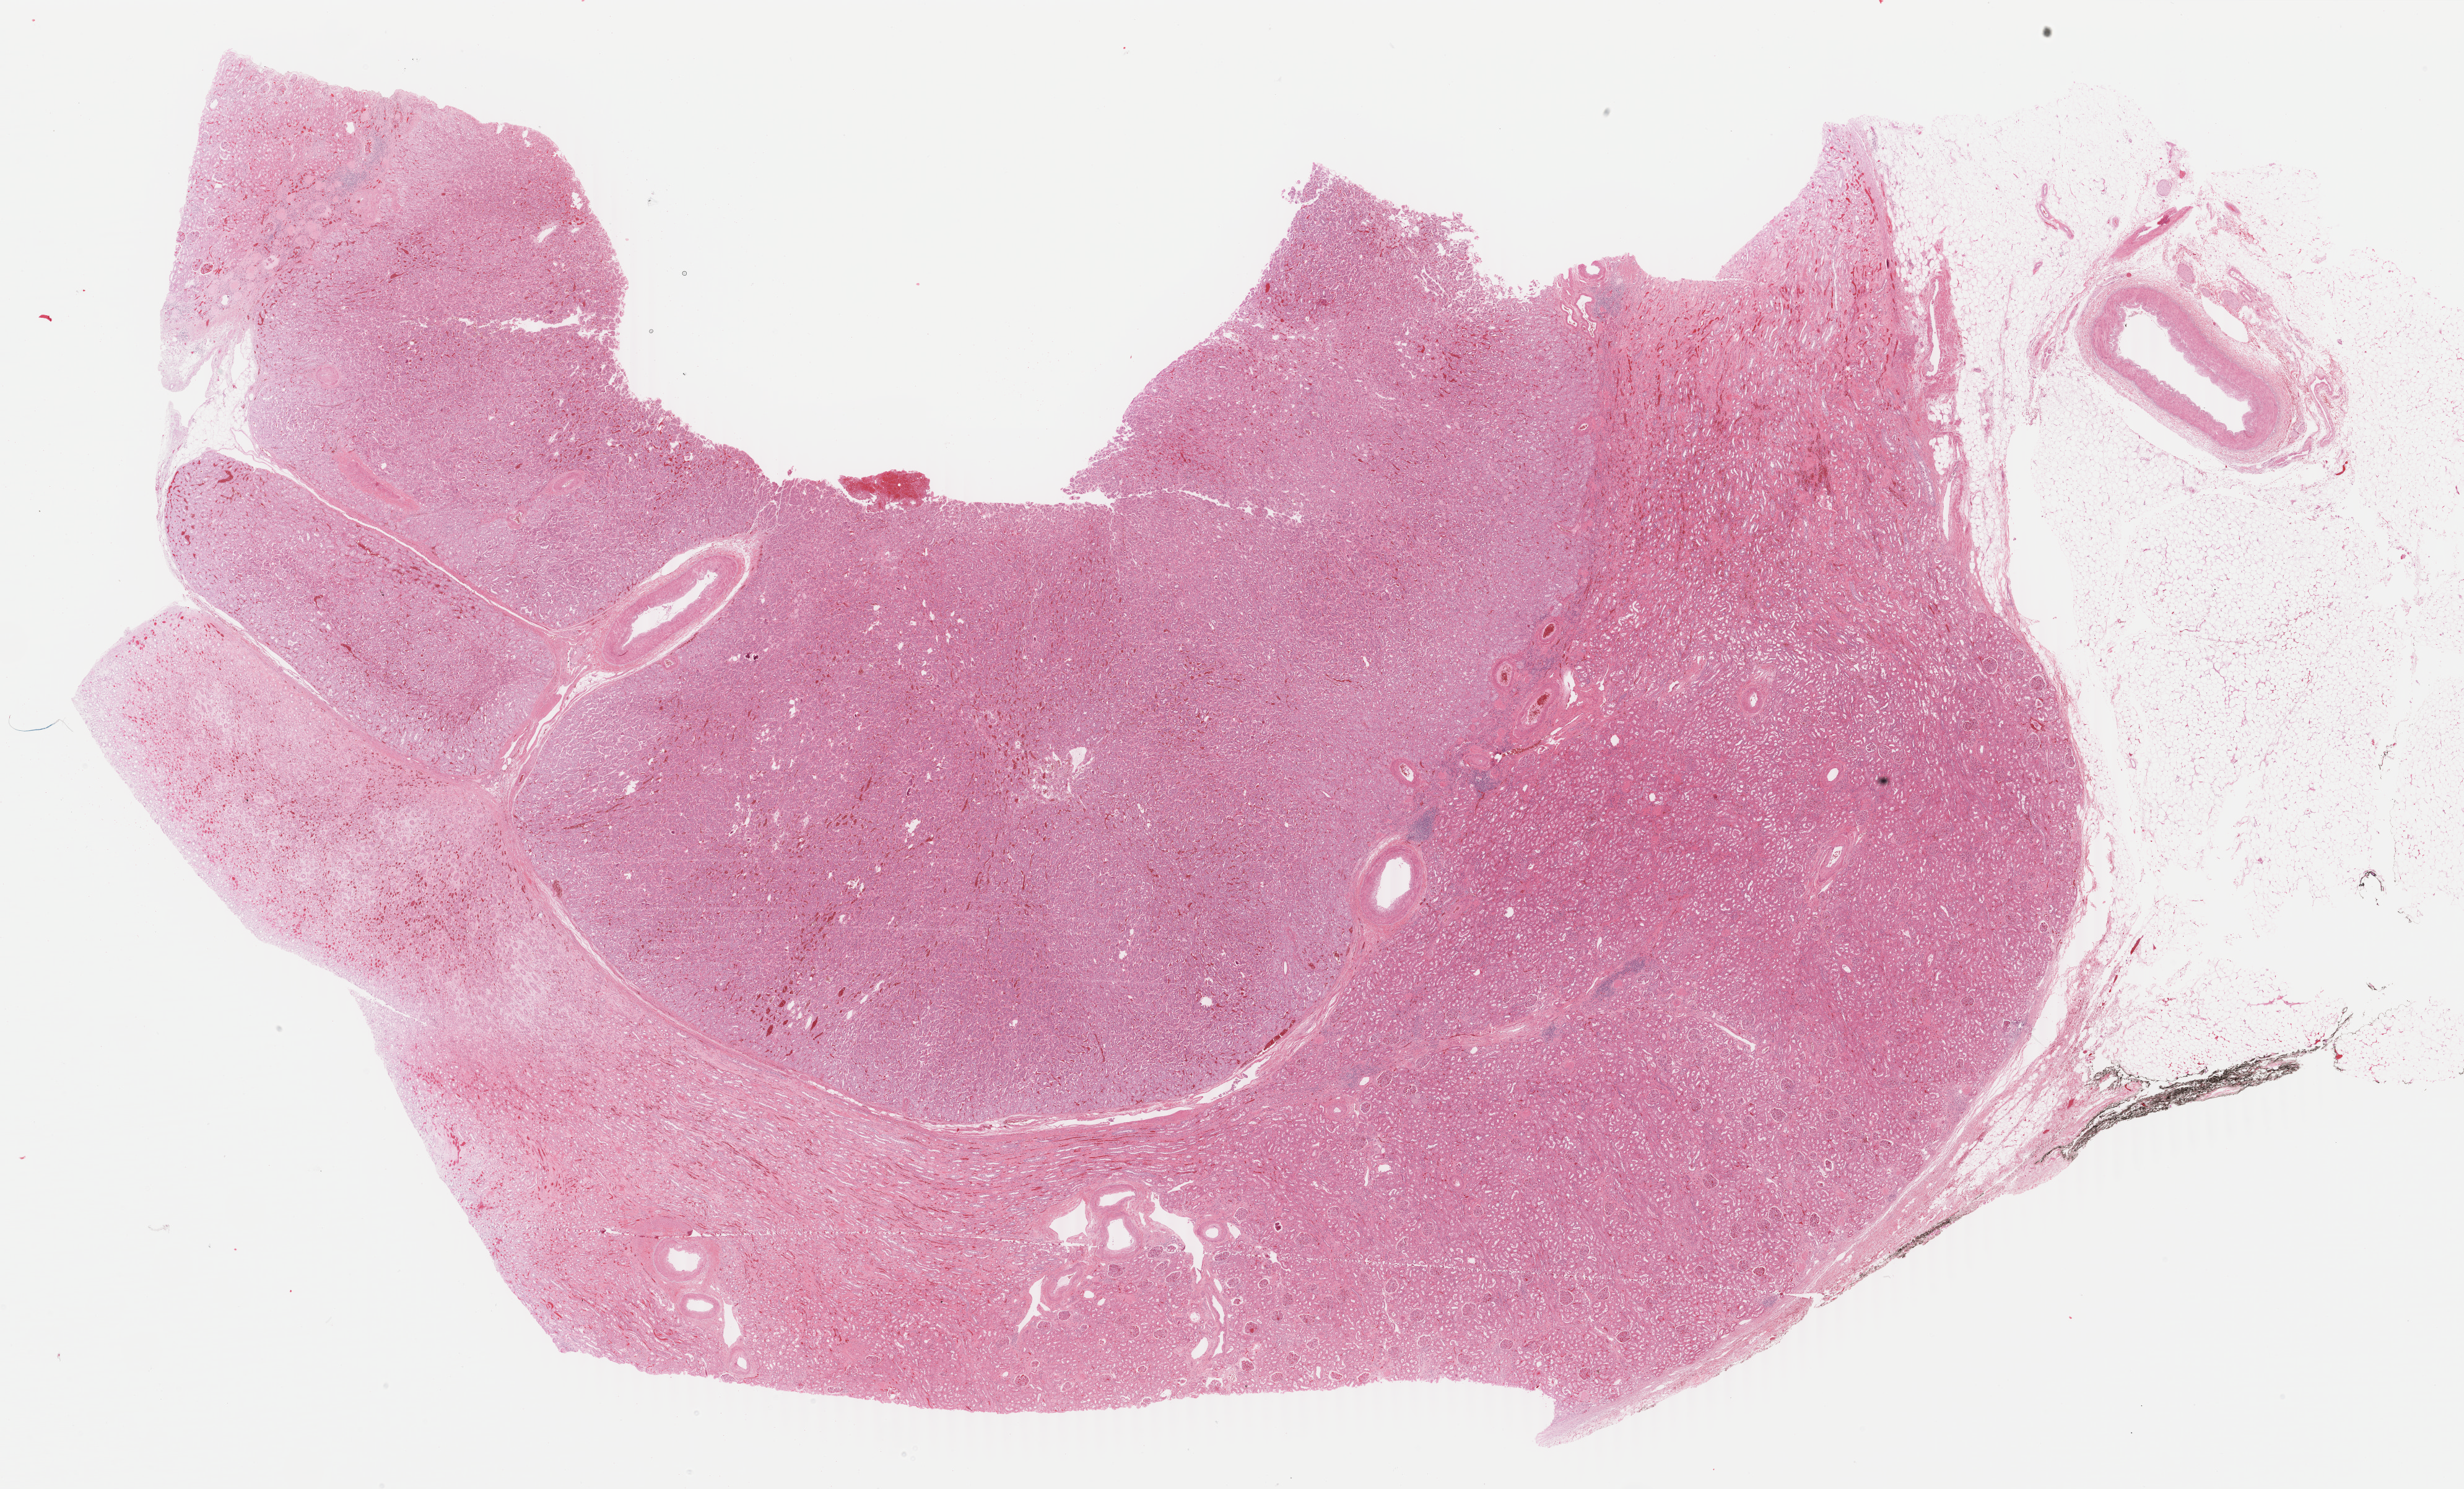
Whole-slide histology image, H&E-stained — shown as a low-resolution overview of the whole scanned area (about 31.6 x 19.1 mm, slide scanned at 40x). Formalin-fixed paraffin-embedded (FFPE) diagnostic section. Sample: primary tumour, kidney. Male, age 67 years at initial diagnosis.
Histologic diagnosis: Renal cell carcinoma, chromophobe type. Laterality: right. AJCC pathologic stage: I (6th edition). TNM: T1a NX MX.